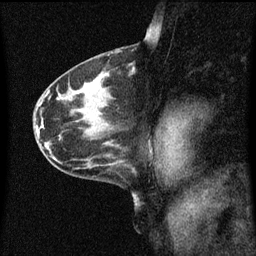
Breast MRI (dynamic contrast-enhanced), one sagittal slice. Position 35 of 60 along the scan axis. Dynamic contrast-enhanced series, image 2 of 3 at this slice position (ordered by acquisition). 1.5 T. TE 4.2 ms, TR 8.4 ms. 2 mm slice thickness. 256 × 256 image matrix, field of view 200 × 200 mm. Female patient, age 41 years.
Structures marked on this image (semi-automatic segmentation, software-assisted and operator-edited):
- analysis volume of interest (the breast-tissue region the enhancement analysis was run in; not a lesion): bounding box <121,58,138,83> (left, top, right, bottom; pixels)
- tumour enhancement mask (voxels above the 70 % enhancement threshold inside the analysis volume of interest): <128,64,136,77>